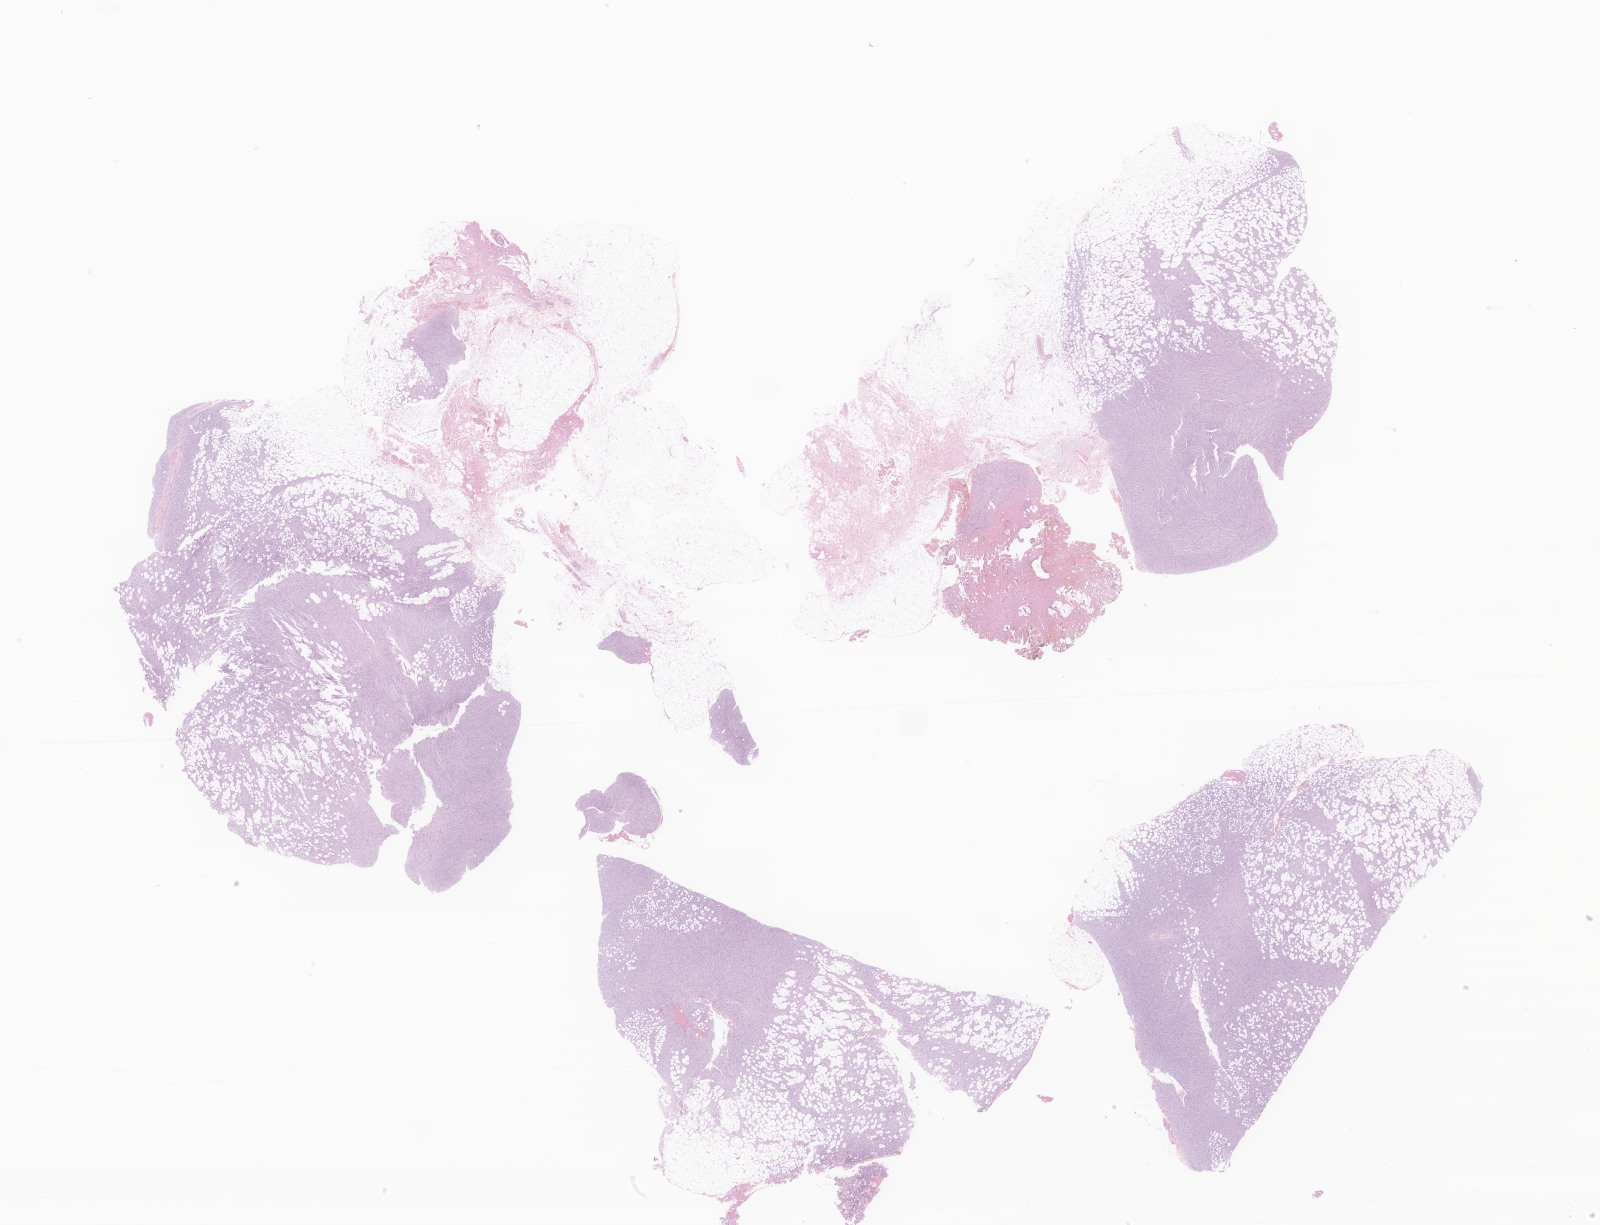
Hematoxylin and eosin (H&E) whole-slide image of tumor tissue from the soft tissue of abdomen — low-resolution overview of the scanned area, about 27.0 x 20.7 mm. Formalin-fixed paraffin-embedded section. Female patient, age 186 months.
• diagnosis (ICD-O-3 morphology term): Pigmented dermatofibrosarcoma protuberans
• tissue or organ of origin (case record): connective, subcutaneous and other soft tissues of abdomen